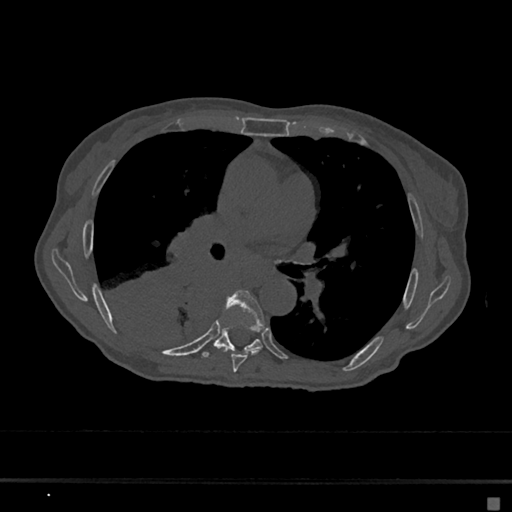
CT including the spine, one axial slice. Slice 397 of 797 in the series (ordered by position). Reconstruction kernel Br40s/3. 120 kVp. Bone window (W 1800 / L 400 HU). 0.5 mm slice thickness. 512 × 512 image matrix. Patient: female, 68 years. From the clinical record (not read from this slice): primary cancer: renal.
Annotated regions visible in this slice (semi-automatic segmentation, software-assisted and operator-edited):
- T6 vertebra: bounding box [x1, y1, x2, y2] px = [224, 290, 265, 372]
- T7 vertebra: [202, 329, 263, 358]